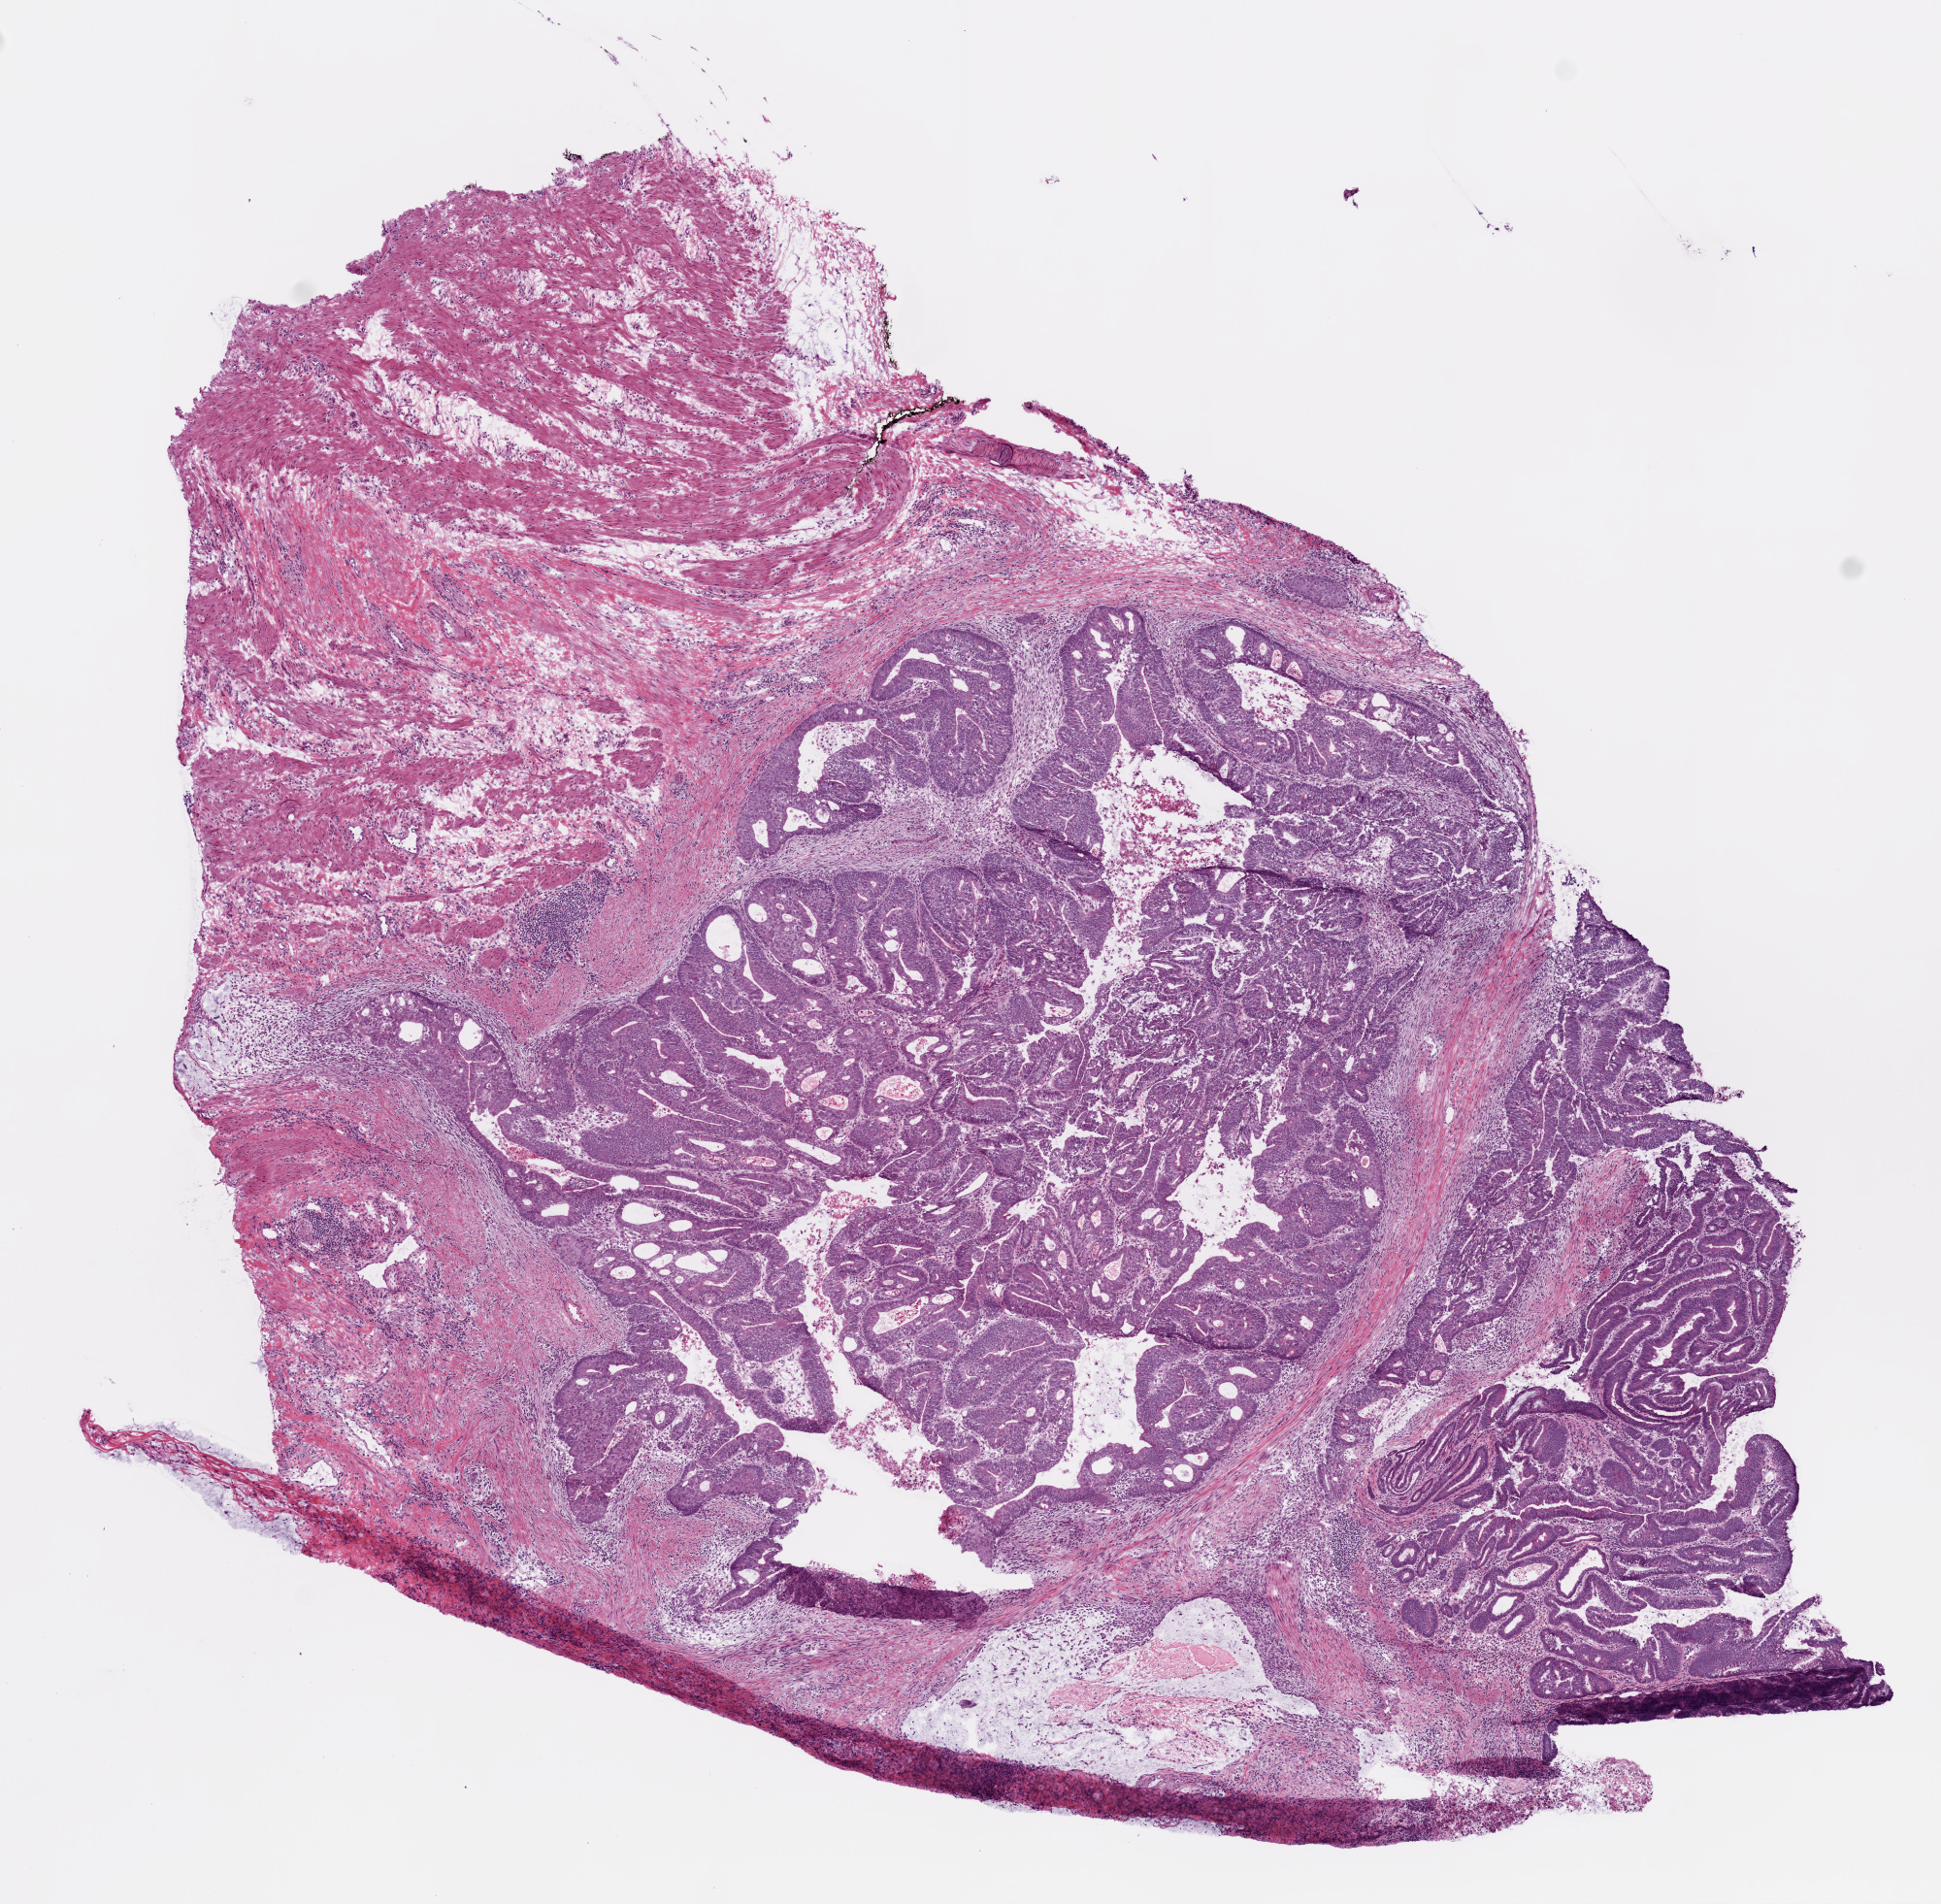
H&E-stained whole-slide image — shown as a low-resolution overview of the whole scanned area (about 8.0 x 7.9 mm); frozen section; colon, primary tumour sample. Male patient; age at initial diagnosis 80 years. Pathologist review of this section (percent, as recorded): tumour cells 66%, tumour nuclei 70%, normal cells 30%, stromal cells 0%, necrosis 4%. Infiltration values recorded for this section: lymphocyte infiltration 20%, monocyte infiltration 1%, neutrophil infiltration 1%.
Pathologic diagnosis: Adenocarcinoma, NOS (ascending colon). AJCC pathologic stage: IIIC (7th edition).